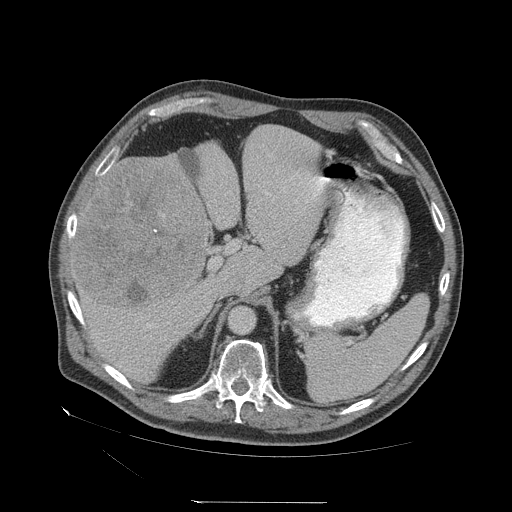
Contrast-enhanced abdominal CT (liver protocol), one axial slice; position 39 of 83 along the scan axis; reconstruction kernel STANDARD; soft-tissue window (W 400 / L 40 HU); 2.5 mm slice thickness; 512 × 512 image matrix. Case-level facts recorded for this patient, not image findings: diagnosis: hepatocellular carcinoma (patient treated with transarterial chemoembolisation; whether this scan precedes or follows treatment is not stated here); TNM stage (as recorded): Stage-I; Child-Pugh class: A; tumour differentiation: well differentiated; tumour nodularity: uninodular.
Structures marked on this image (semi-automatically segmented with operator editing):
- liver parenchyma outside the tumour (the mass and vessels are separate outlines, so this box may not span the whole liver): bounding box (x1, y1, x2, y2) in pixels: (70, 126, 324, 382)
- mass: (75, 159, 209, 310)
- liver vessels: (82, 177, 325, 326)